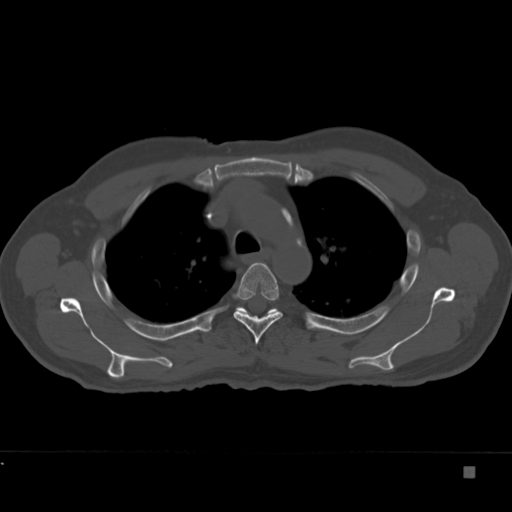
CT including the spine, one axial slice; position 269 of 332 along the scan axis; reconstruction kernel Br40s; 120 kVp; bone window (W 1800 / L 400 HU); 1.5 mm slice thickness; 512 × 512 image matrix, field of view 389 × 389 mm. Male patient, age 72 years. From the clinical record (not read from this slice): primary cancer: skeletal.
Annotated regions visible in this slice (semi-automatic segmentation, software-assisted and operator-edited):
- T4 vertebra: bounding box [x1, y1, x2, y2] px = [233, 263, 283, 345]
- T5 vertebra: [236, 307, 275, 313]